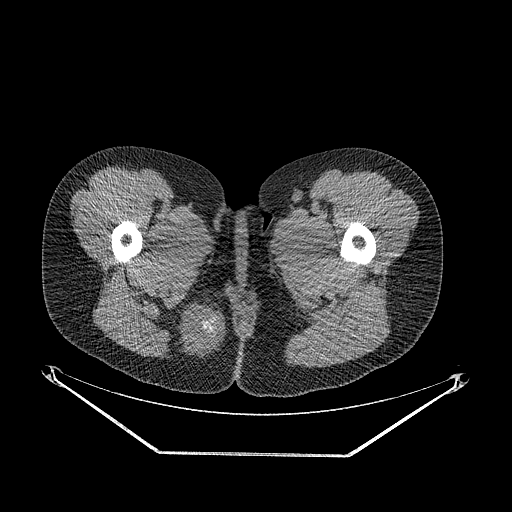
CT of an extremity soft-tissue mass (from a PET/CT study), one axial slice. Slice 28 of 267 in the series (ordered by position). 120 kVp. Soft-tissue window (W 400 / L 40 HU). 512 × 512 image matrix, field of view 500 × 500 mm. Female patient. Case-level facts recorded for this patient, not image findings: histological type: epithelioid sarcoma; grade: intermediate; site of the primary tumour: right buttock.
Annotated regions visible in this slice (expert contour drawn on MRI and transferred to this co-registered scan by the dataset authors):
- gross tumour volume including surrounding oedema: box from (x=171, y=299) to (x=225, y=359) px
- gross tumour volume (mass): (x=176, y=304)–(x=225, y=353)